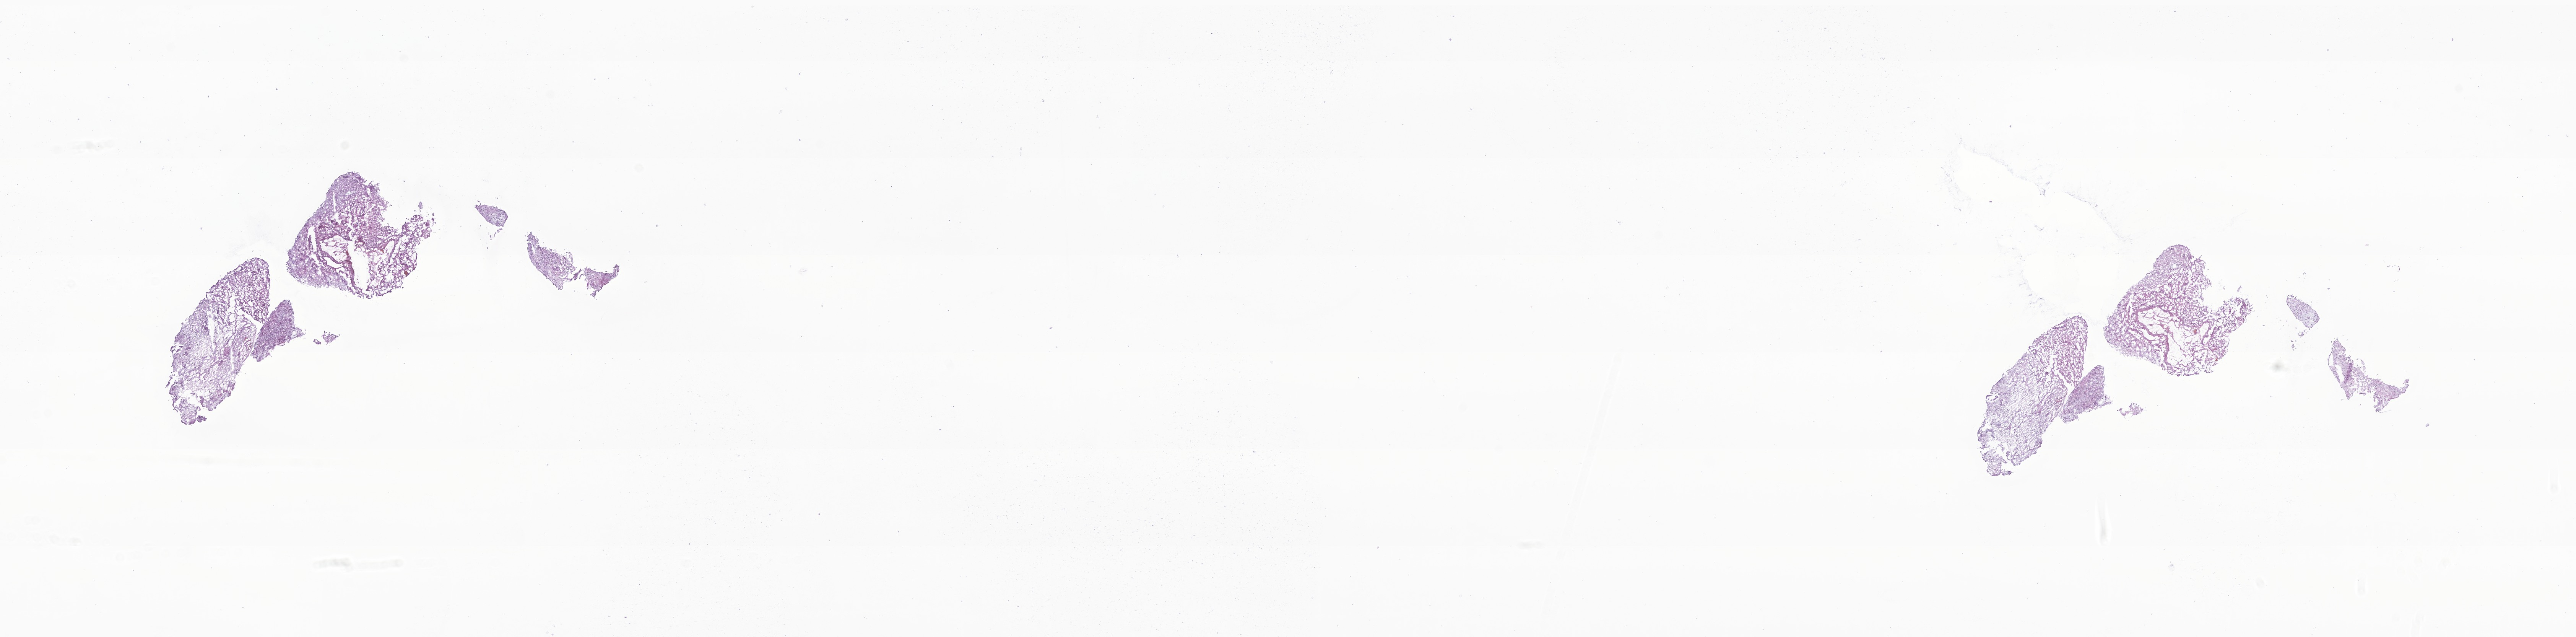
Hematoxylin and eosin (H&E) whole-slide image of tumor tissue from the brain, a low-resolution overview of the entire scanned area, about 28.4 x 7.0 mm; frozen section (OCT-embedded). Patient: female, age 159 months (13 years 3 months).
* recorded diagnosis: Pilocytic astrocytoma